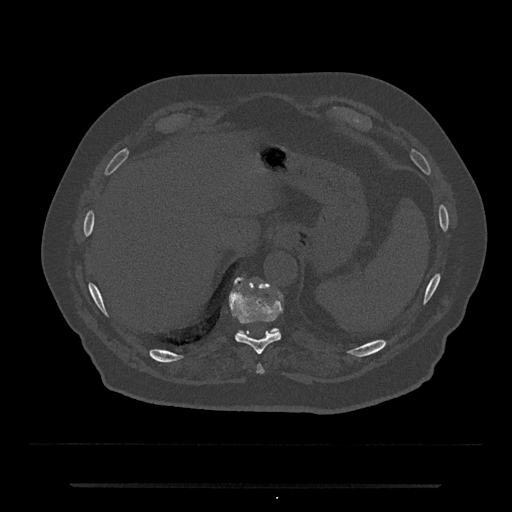
CT including the spine, one axial slice; position 695 of 797 along the scan axis; reconstruction kernel Br40s/3; bone window (W 1800 / L 400 HU); 0.5 mm slice thickness; 512 × 512 image matrix, field of view 434 × 434 mm. Patient: male, 80 years. Case-level facts recorded for this patient, not image findings: primary cancer: prostate; vertebrae with lytic lesions (as recorded): L1, T11.
Outlined on this slice (semi-automatically segmented with operator editing):
- T10 vertebra: box from (x=229, y=278) to (x=282, y=355) px
- T11 vertebra: (x=240, y=327)–(x=280, y=333)
- T9 vertebra: (x=257, y=365)–(x=264, y=374)